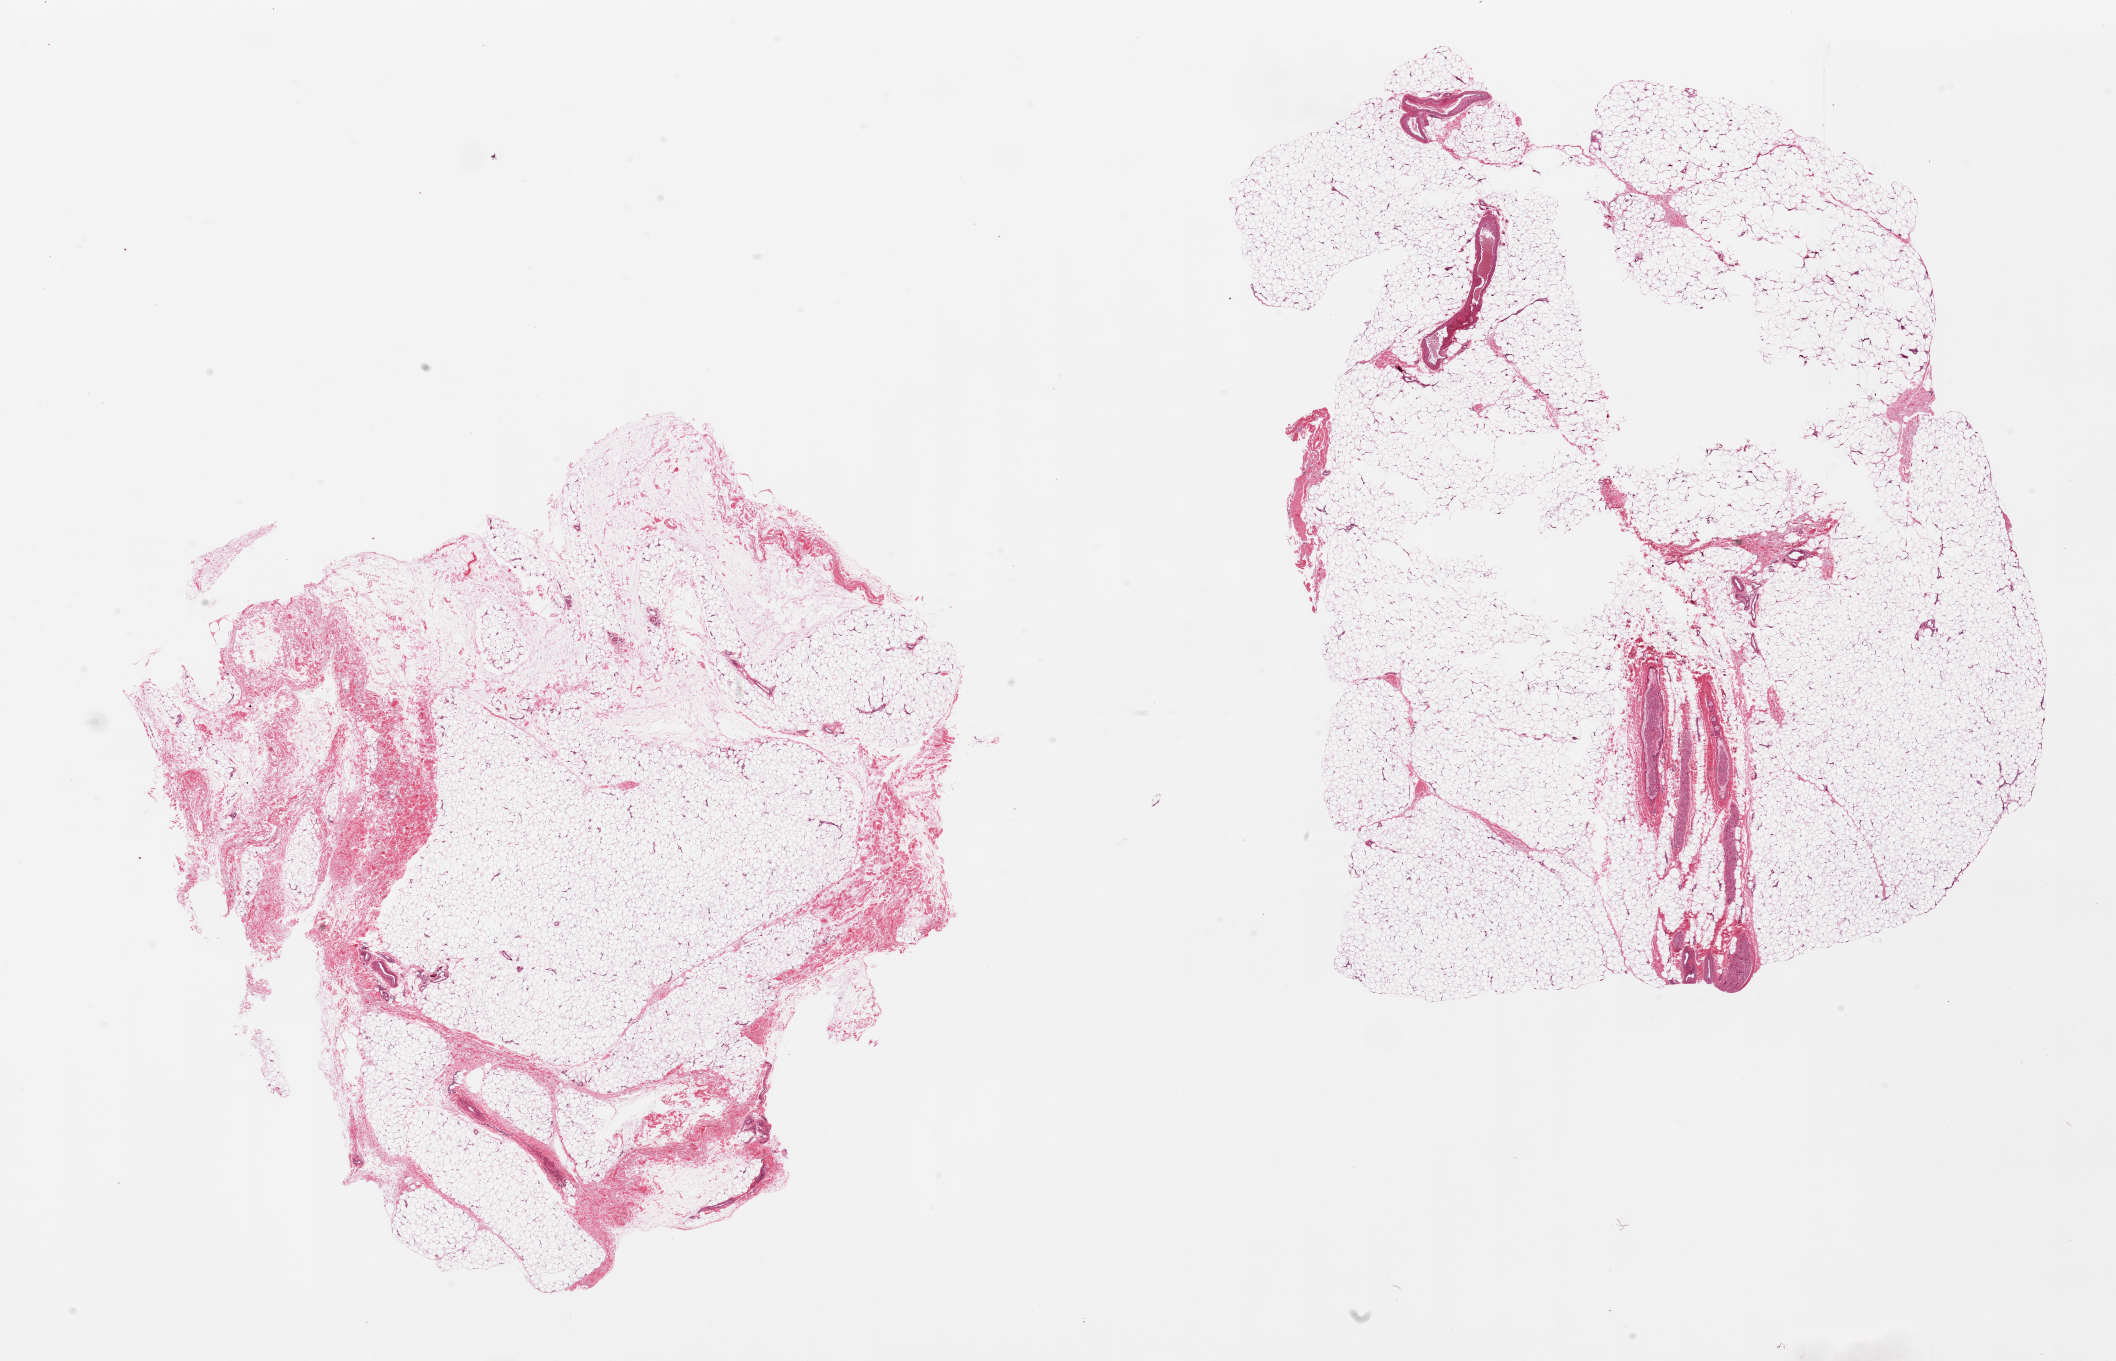
Haematoxylin and eosin whole-slide image, brightfield, low-resolution overview of the scanned area, about 33.5 x 21.5 mm (acquisition: 20x scan), PAXgene-fixed paraffin-embedded (PFPE) section, target tissue: adipose tissue, donor tissue sample. Male donor.
Reviewer comment on this tissue sample: 2 pieces, small portion of nerve (<10% of one piece).